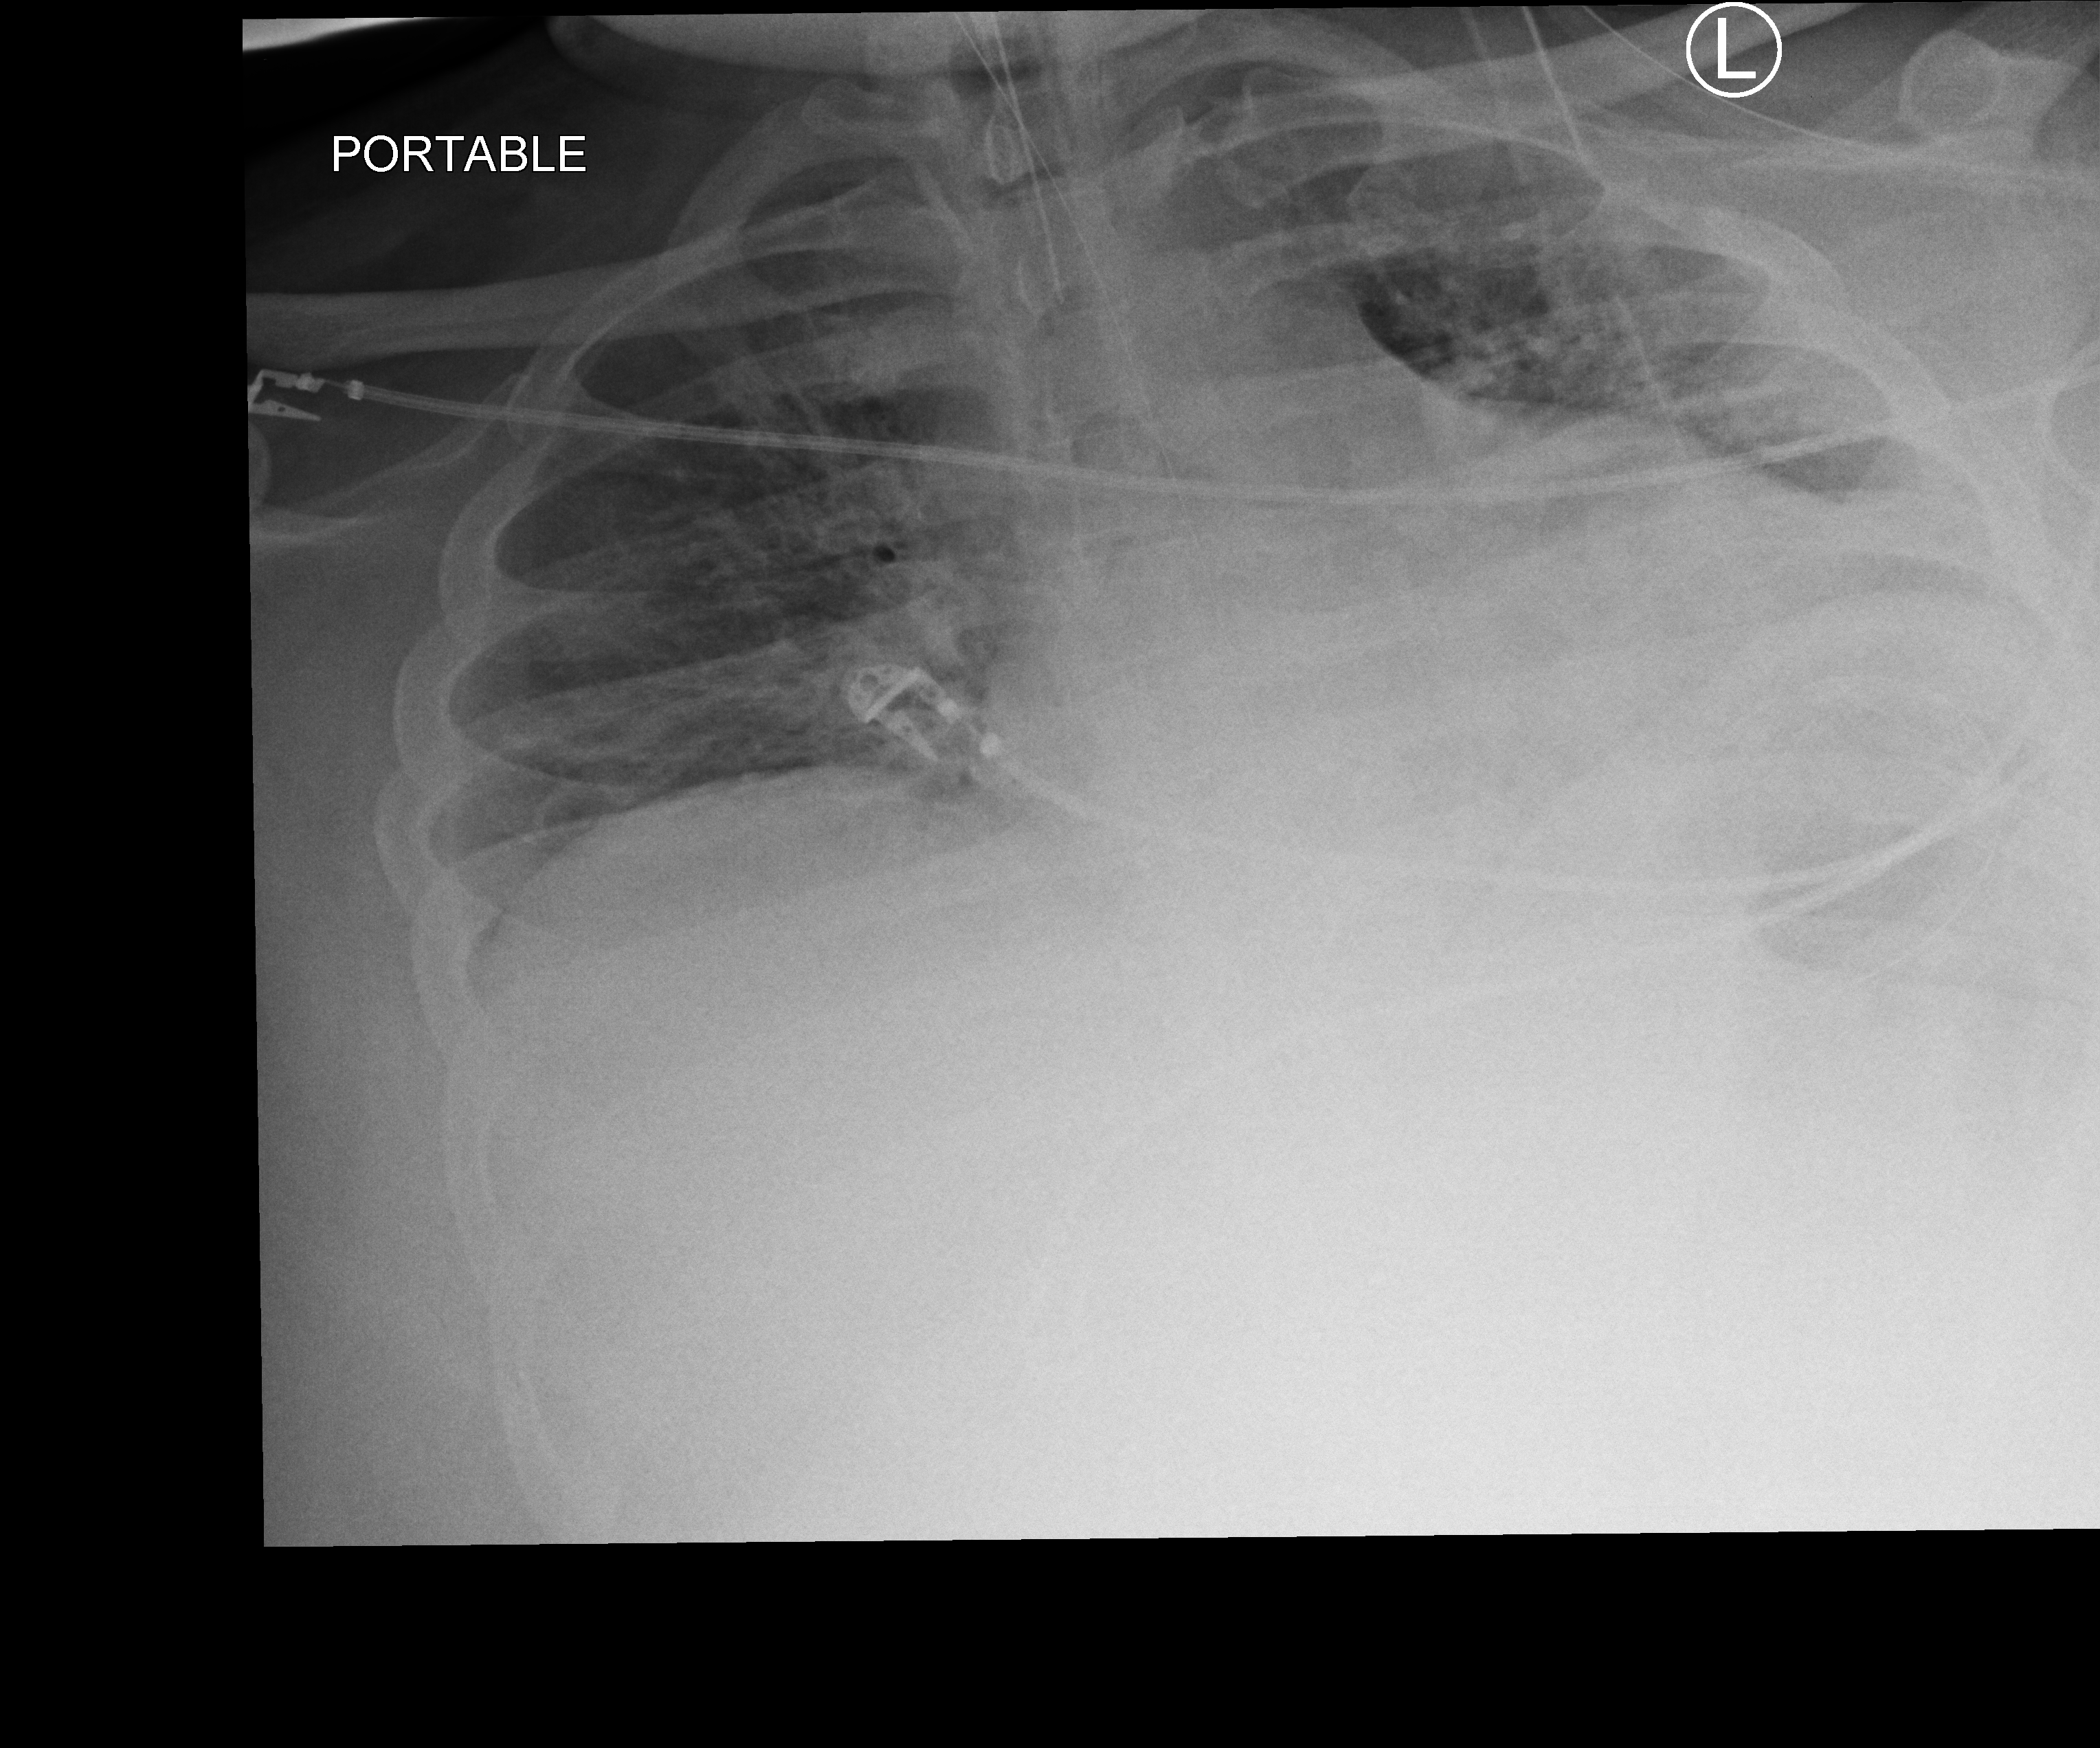
Bedside chest radiograph (computed radiography); anteroposterior (AP) projection. Patient hospitalised with COVID-19; male, aged 18–59 years.
Hospital-stay facts (about this admission, not read from this image; timing relative to this image not recorded):
- admitted to intensive care during this hospital stay: yes